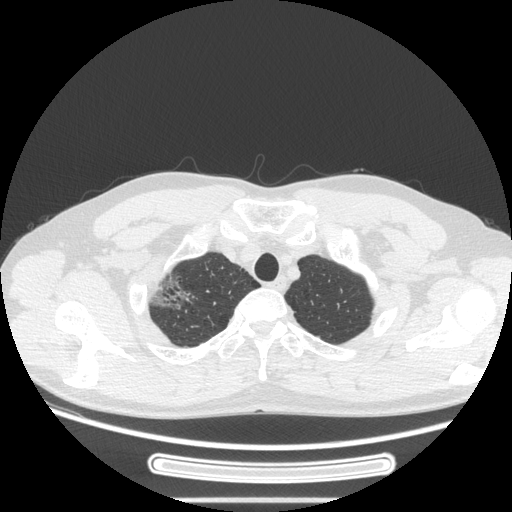
Chest CT, one axial slice; slice 233 of 269 in the series (ordered by position); 120 kVp; lung window (W 1500 / L -600 HU); 512 × 512 image matrix, field of view 382 × 382 mm. Male patient, age 53 years. From the clinical record (not read from this slice): clinical TNM (as recorded): T1c N0 M0.
Structures marked on this image (bounding box drawn by a radiologist):
- lung tumour (recorded histology: adenocarcinoma): bounding box (x1, y1, x2, y2) in pixels: (145, 267, 201, 323)